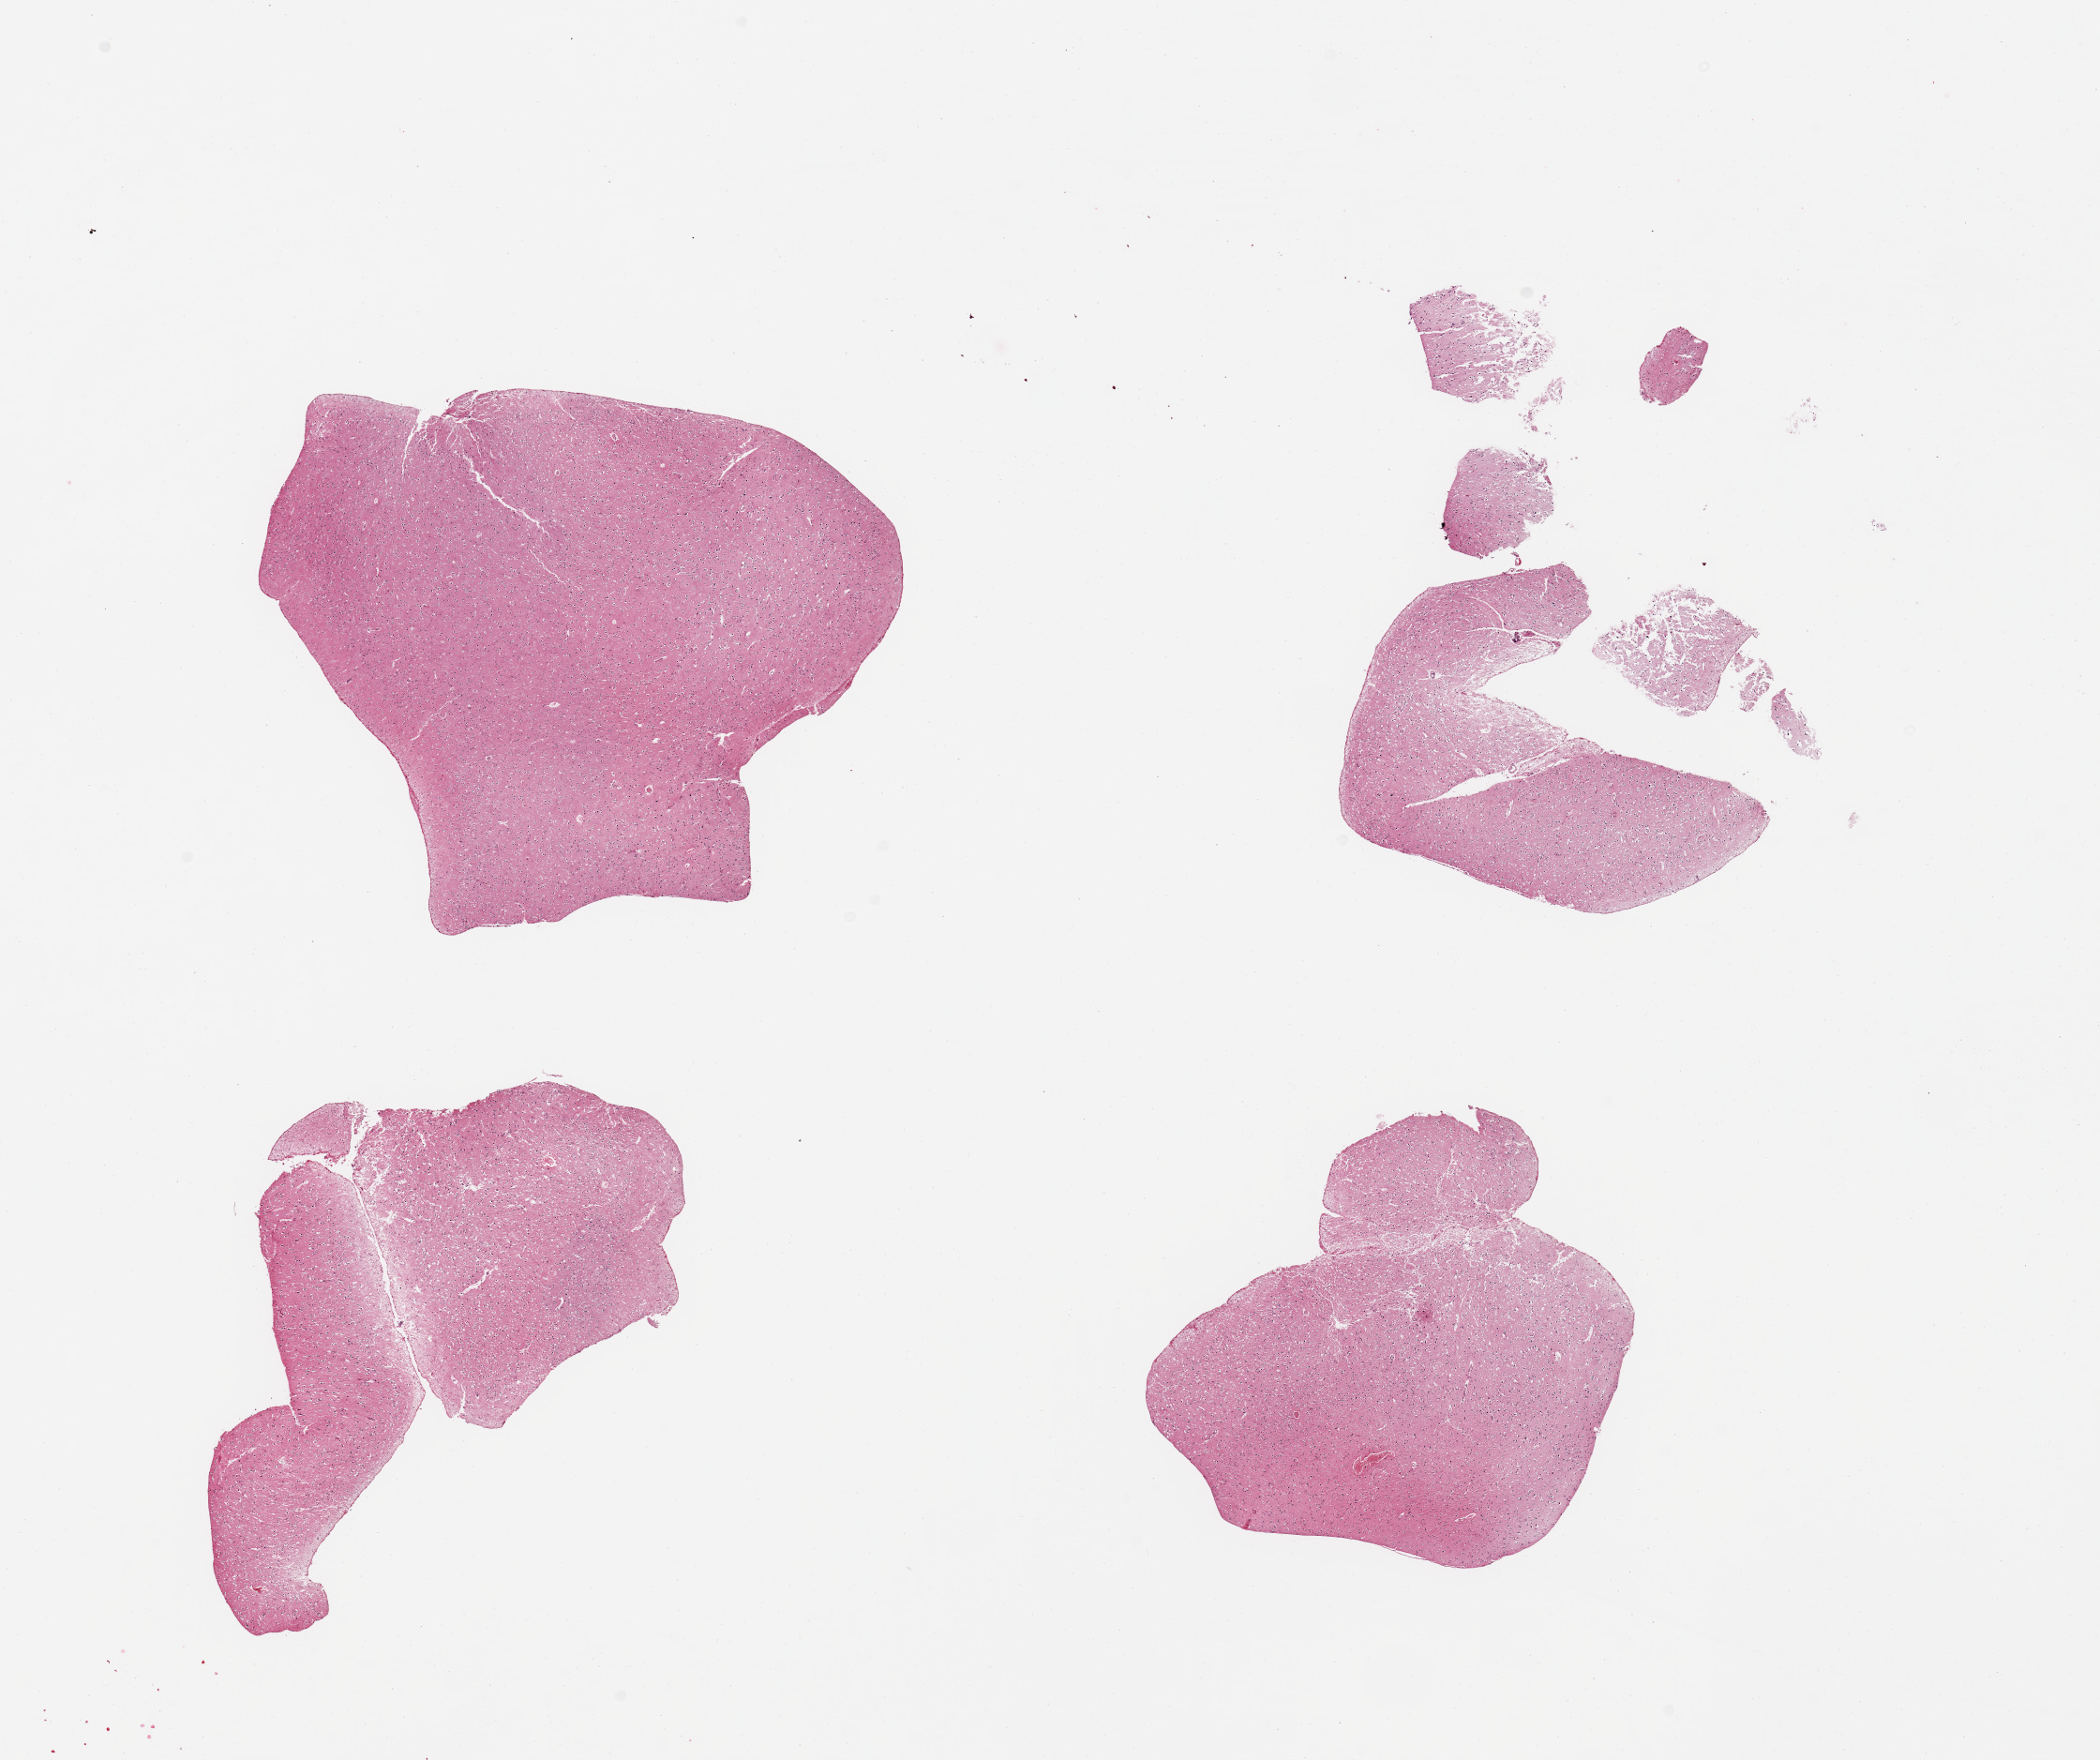
Digitized hematoxylin and eosin (H&E)-stained section — shown as a low-resolution overview of the whole scanned area (about 17.7 x 14.8 mm), PAXgene-fixed, paraffin-embedded tissue, target tissue: cerebral cortex, donor tissue sample. Donor: female.
Review note (as recorded): 4 fragmented pieces.